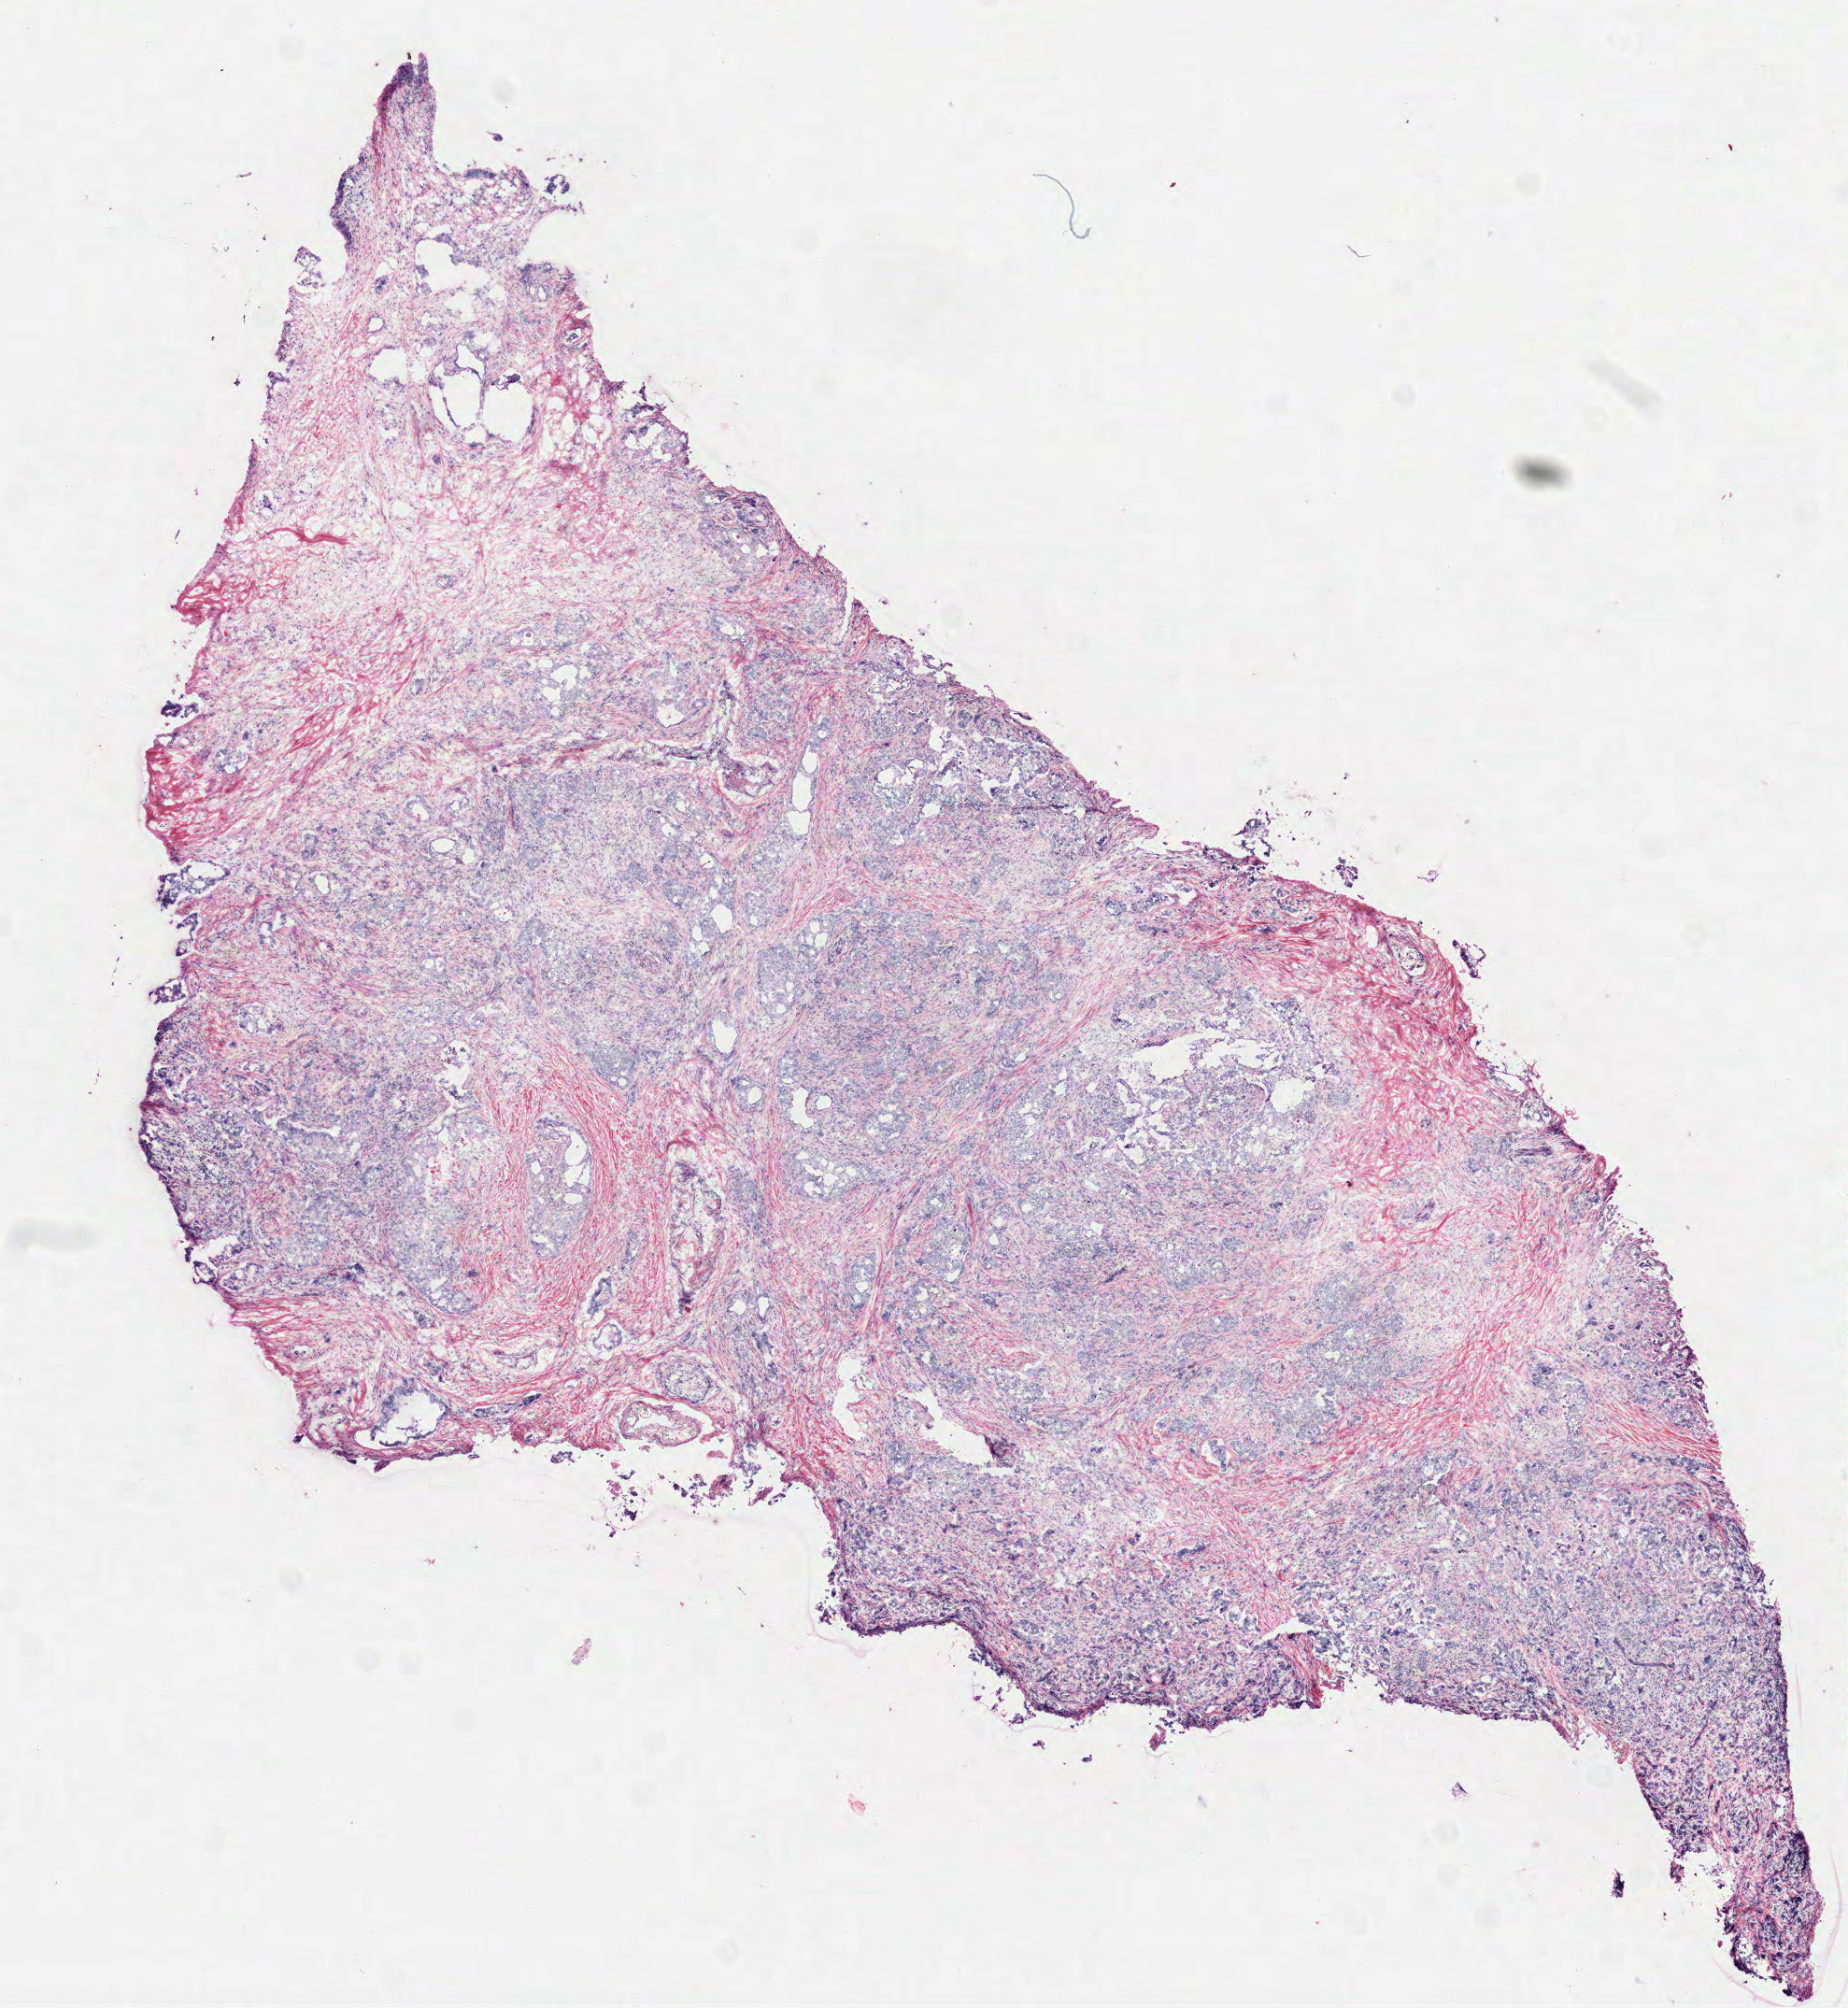
Hematoxylin and eosin (H&E) stained whole-slide image, a low-resolution overview of the entire scanned area, about 8.0 x 8.7 mm, frozen section from the top of the tissue portion, pancreas, primary tumour sample. Female patient; age at initial diagnosis 64 years.
Pathologic diagnosis: Infiltrating duct carcinoma, NOS (head of pancreas).